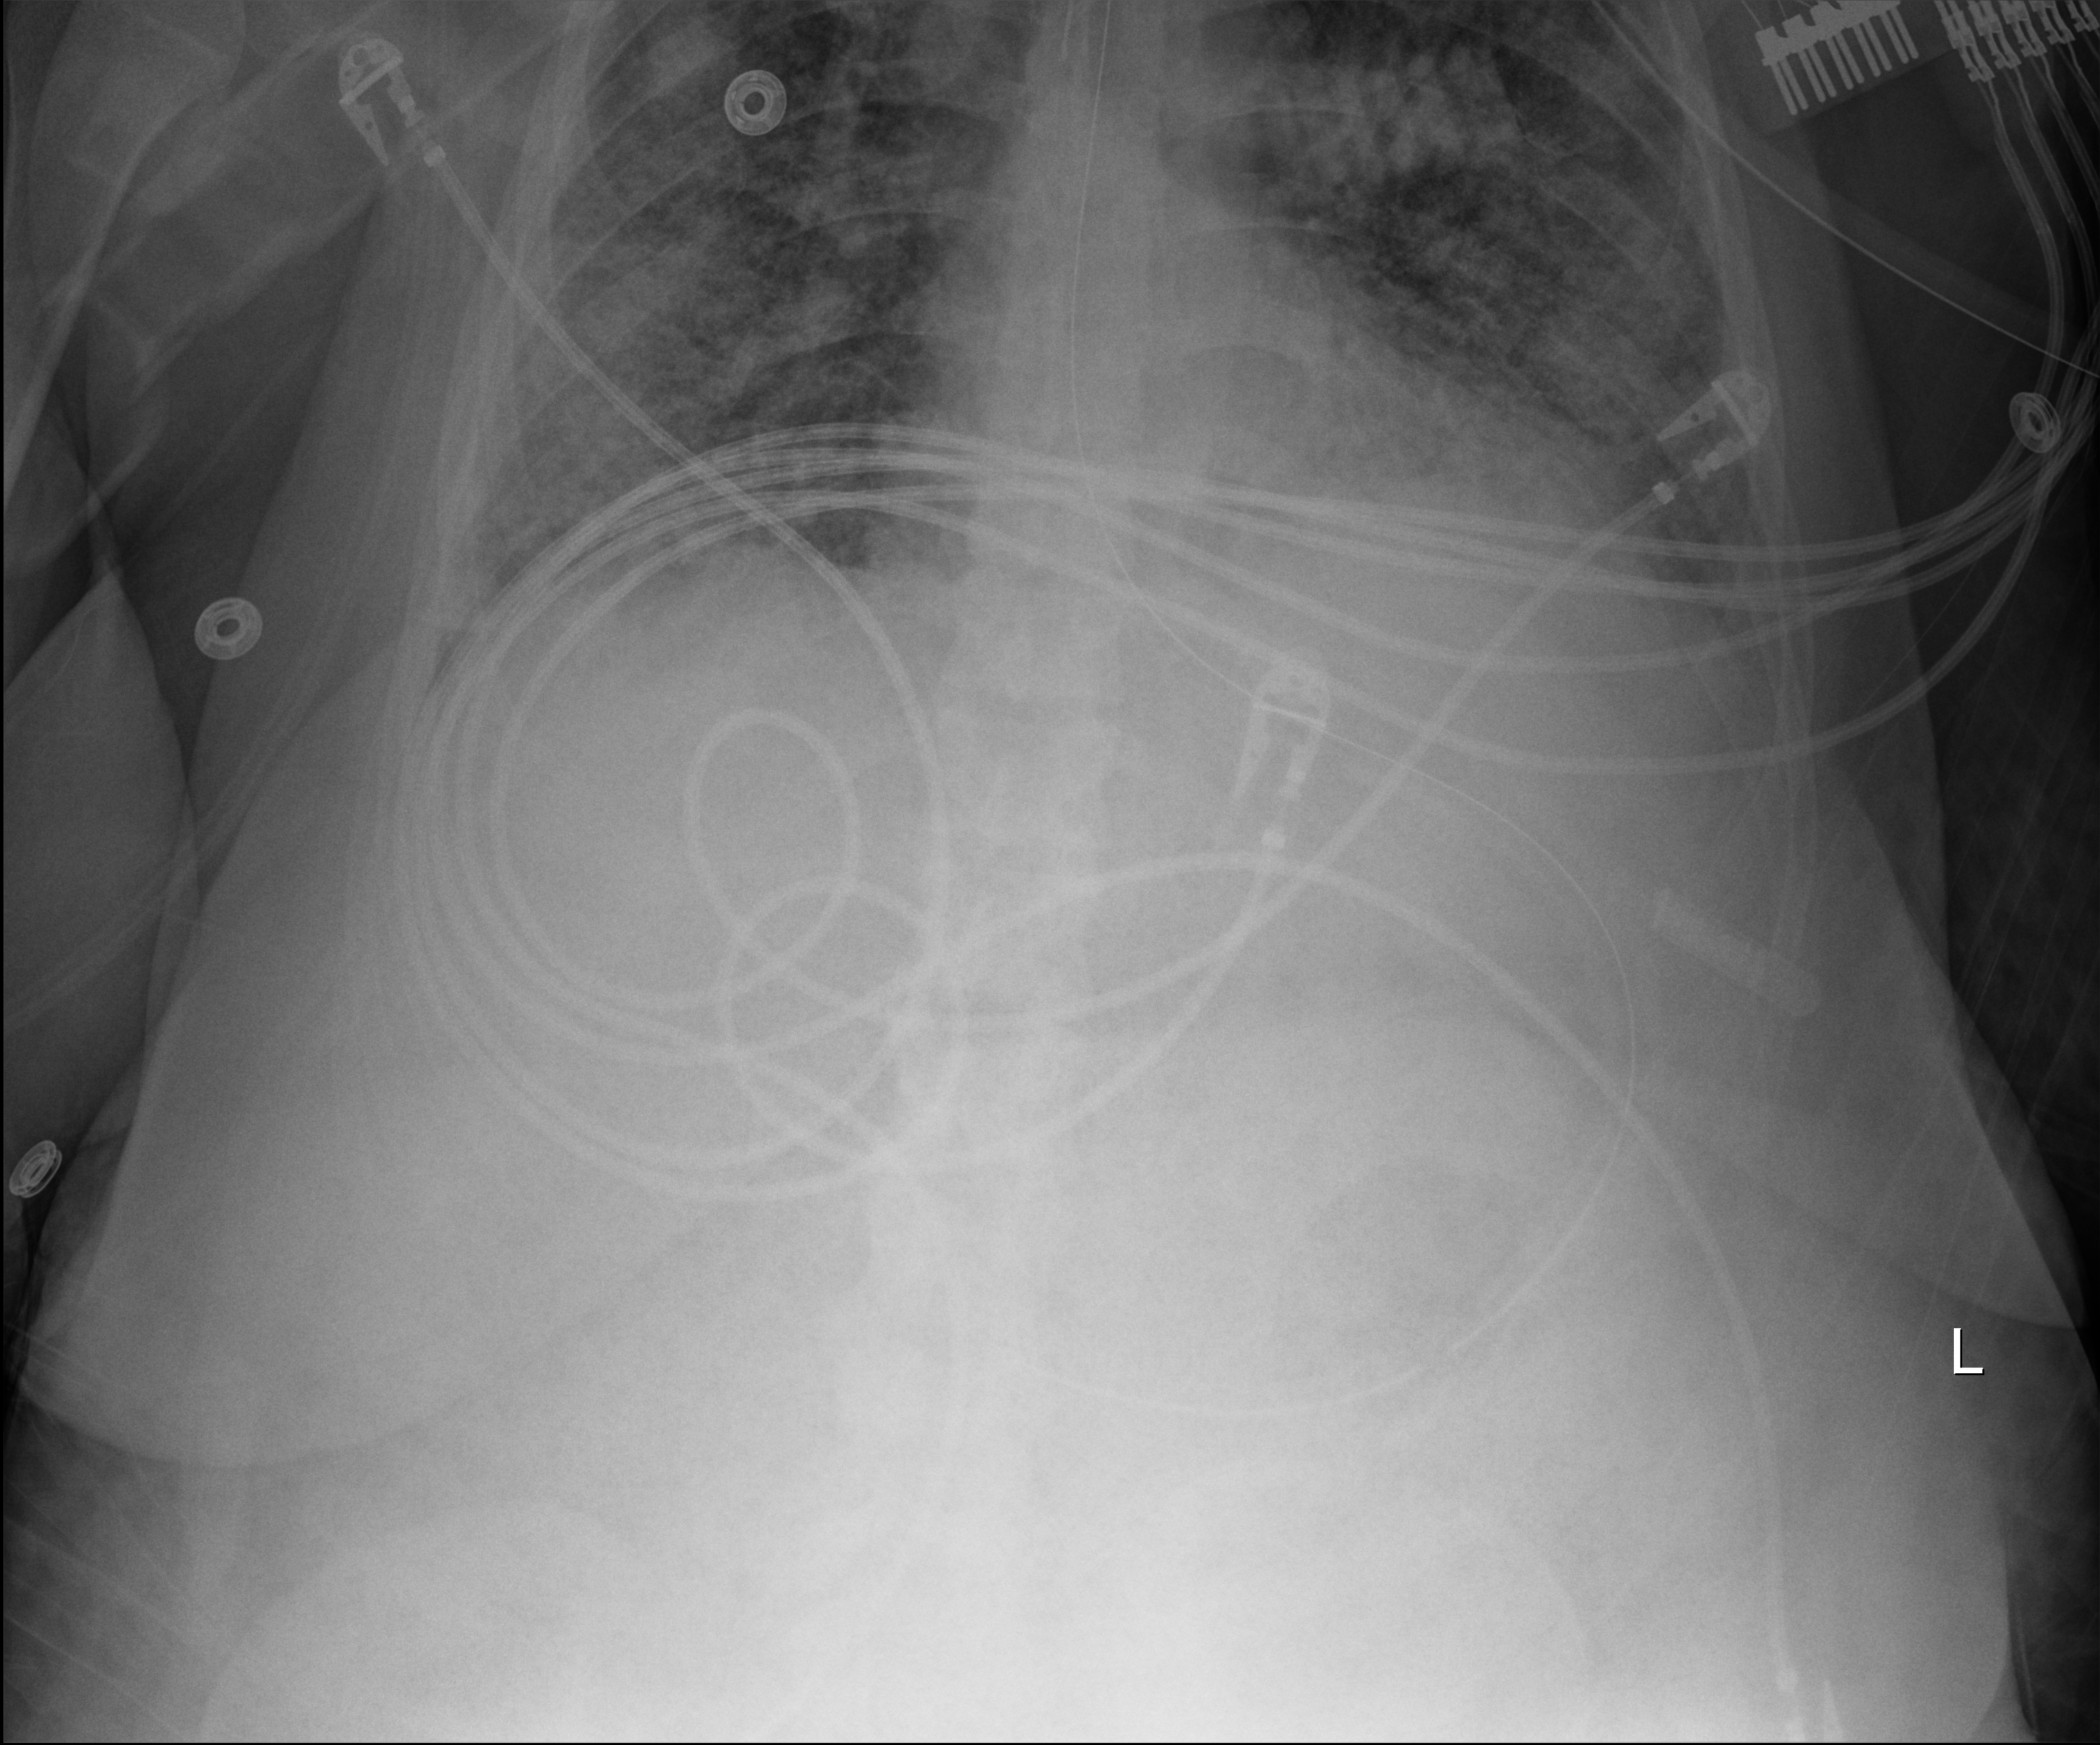
Chest X-ray (portable); anteroposterior (AP) projection. Patient hospitalised with COVID-19; female, aged 18–59 years.
Hospital-stay facts (about this admission, not read from this image; timing relative to this image not recorded):
- mechanically ventilated during this hospital stay: yes
- admitted to intensive care during this hospital stay: no
- length of hospital stay: 33 days